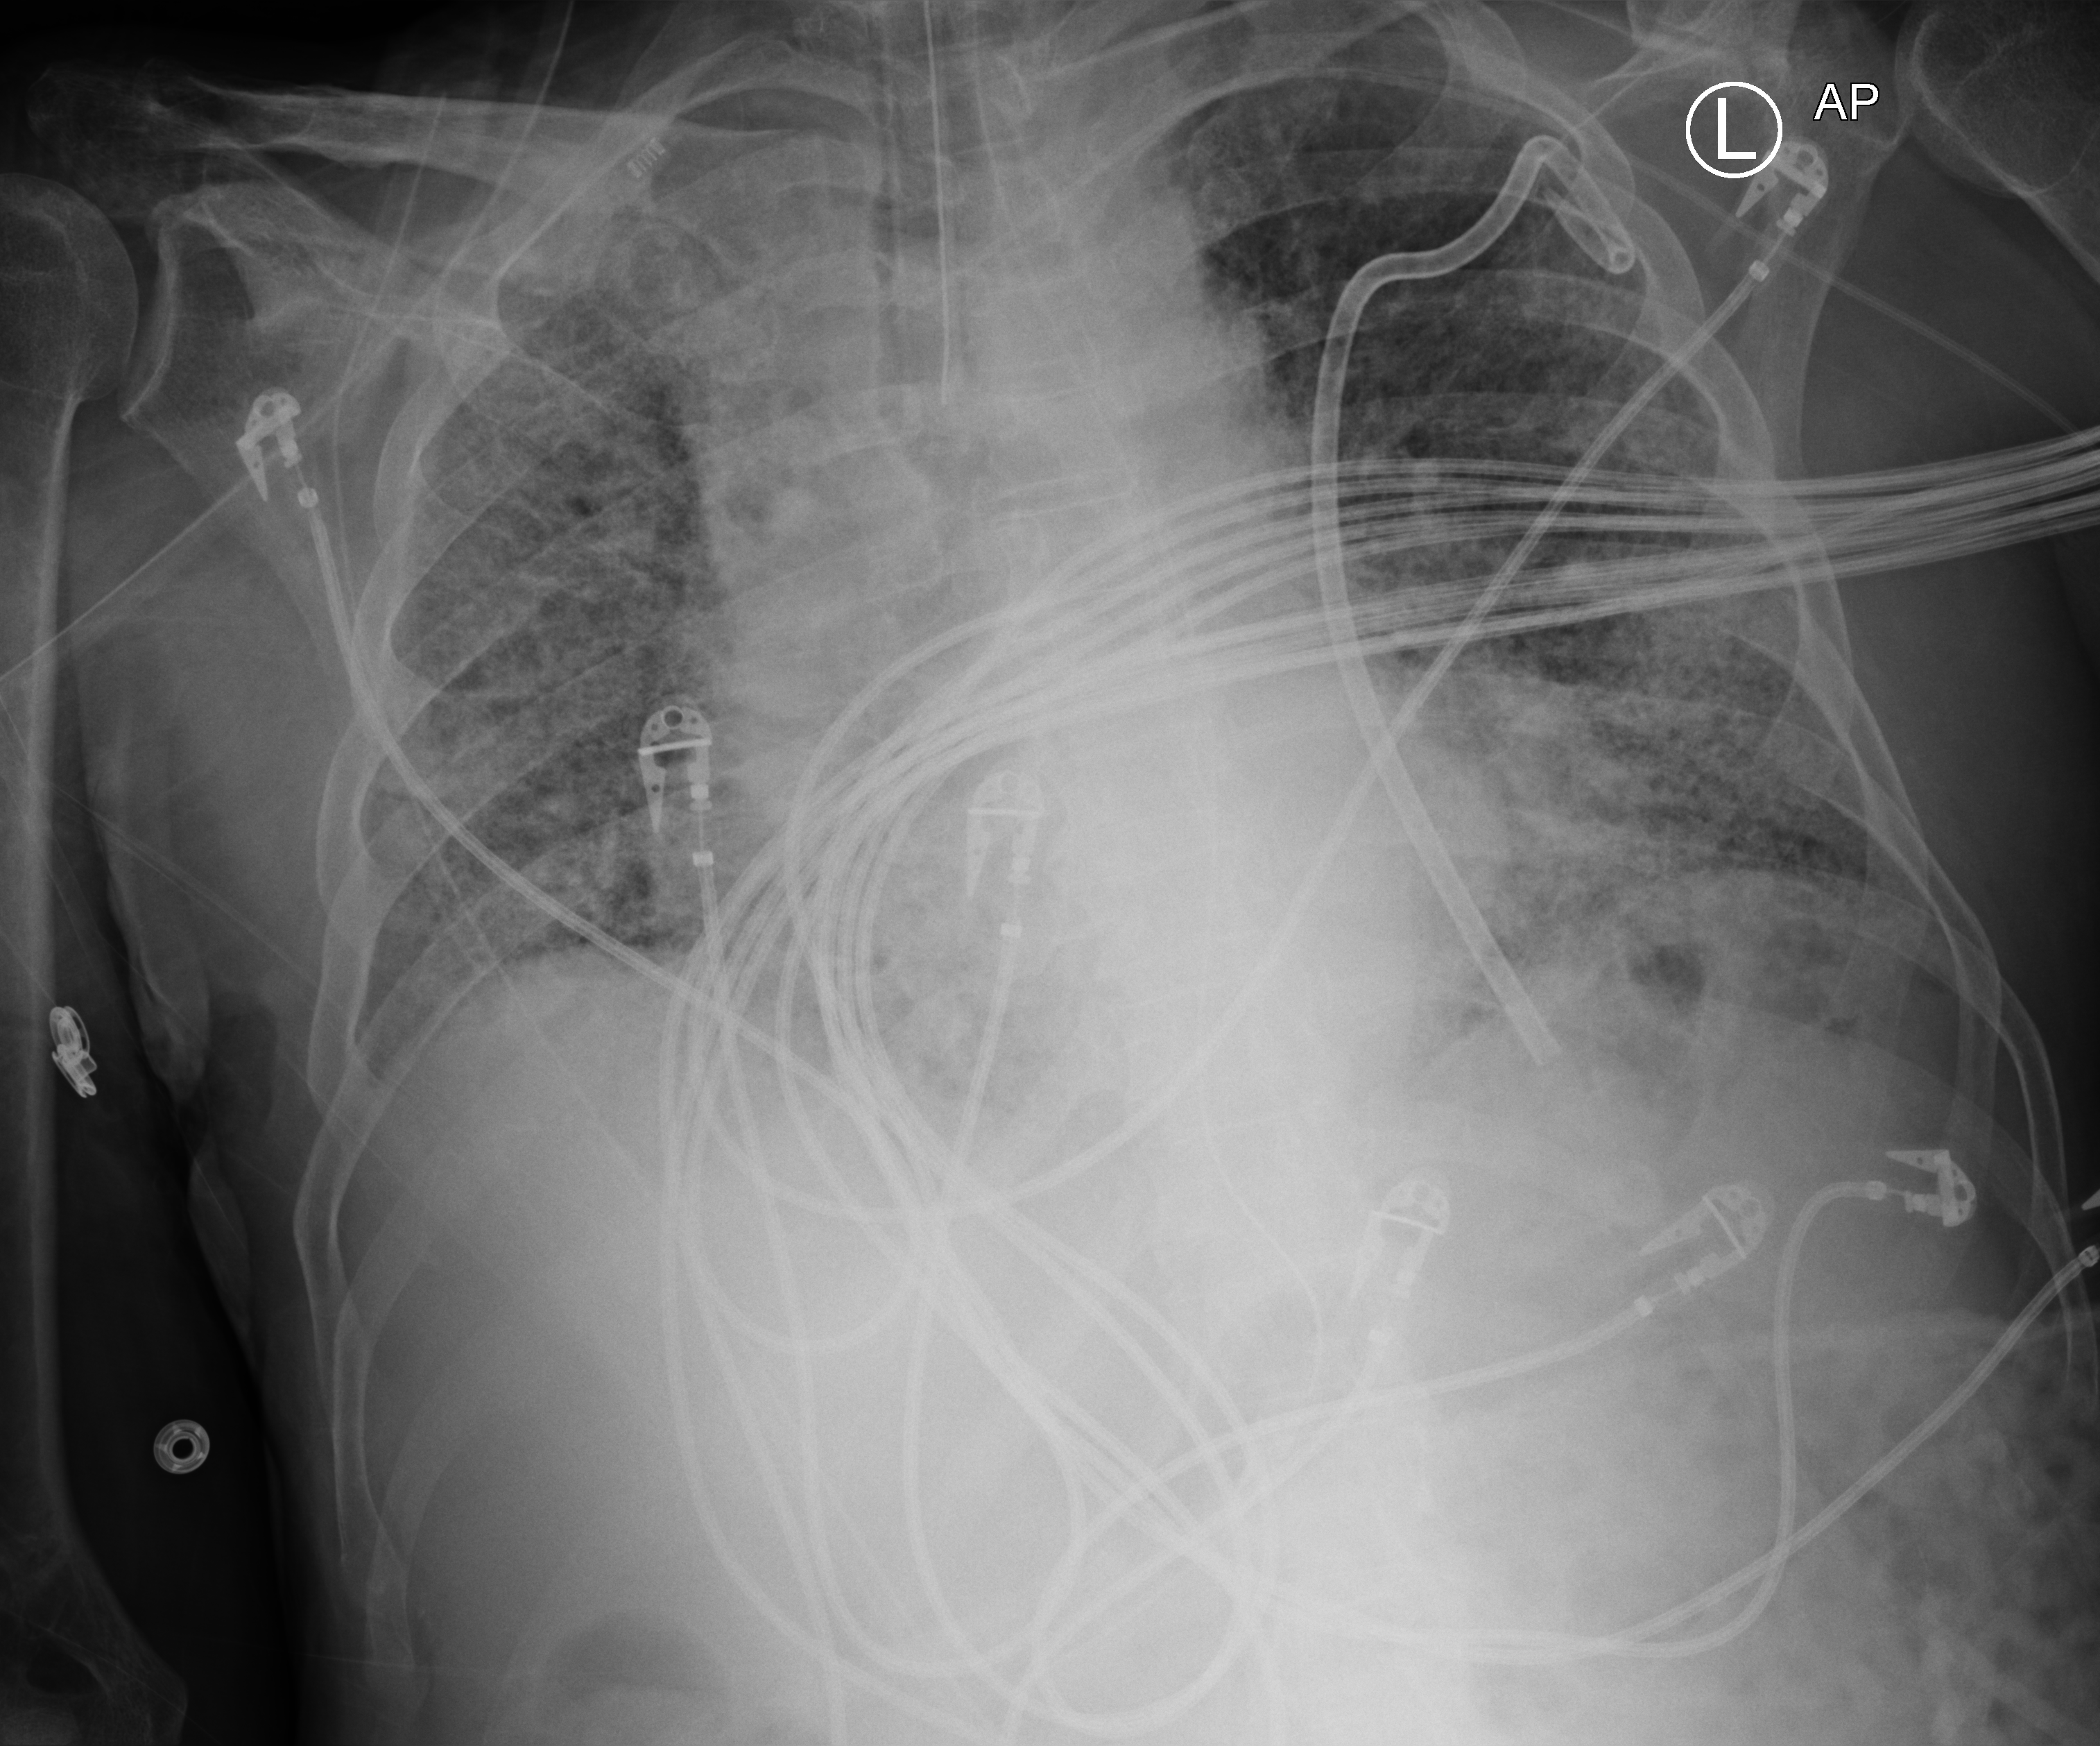
Chest X-ray (portable), anteroposterior (AP) projection. Male patient hospitalised with COVID-19, age 60–74 years.
Admission-level facts for this patient (not findings on this image; timing relative to this image not recorded): mechanically ventilated during this hospital stay: yes; admitted to intensive care during this hospital stay: yes.